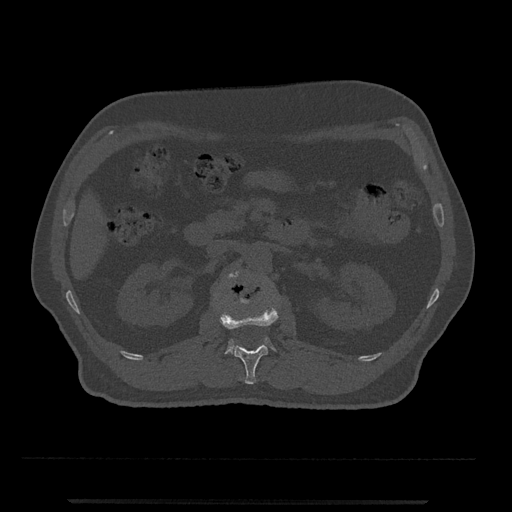
CT including the spine, one axial slice. Position 309 of 797 along the scan axis. Reconstruction kernel Br40s/3. 120 kVp. Bone window (W 1800 / L 400 HU). 512 × 512 image matrix, field of view 419 × 419 mm. Patient: male, 63 years. Case-level facts recorded for this patient, not image findings: primary cancer: prostate.
Annotated regions visible in this slice (semi-automatically segmented with operator editing):
- L1 vertebra: bounding box (x1, y1, x2, y2) in pixels: (220, 297, 279, 384)
- L2 vertebra: (225, 272, 276, 354)